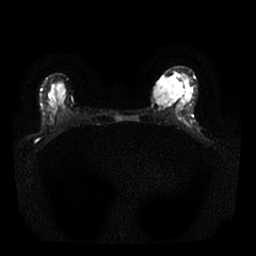
Breast MRI, one axial slice. Slice 13 of 25 in the series (ordered by position). Diffusion-weighted series; image 2 of 4 stored at this slice position (different b-values; order by instance number). 1.5 T. 4 mm slice thickness. 256 × 256 image matrix, field of view 310 × 310 mm. Female patient.
Outlined on this slice (manually delineated by an expert):
- tumour on diffusion-weighted imaging: bounding box <154,77,181,106> (left, top, right, bottom; pixels)